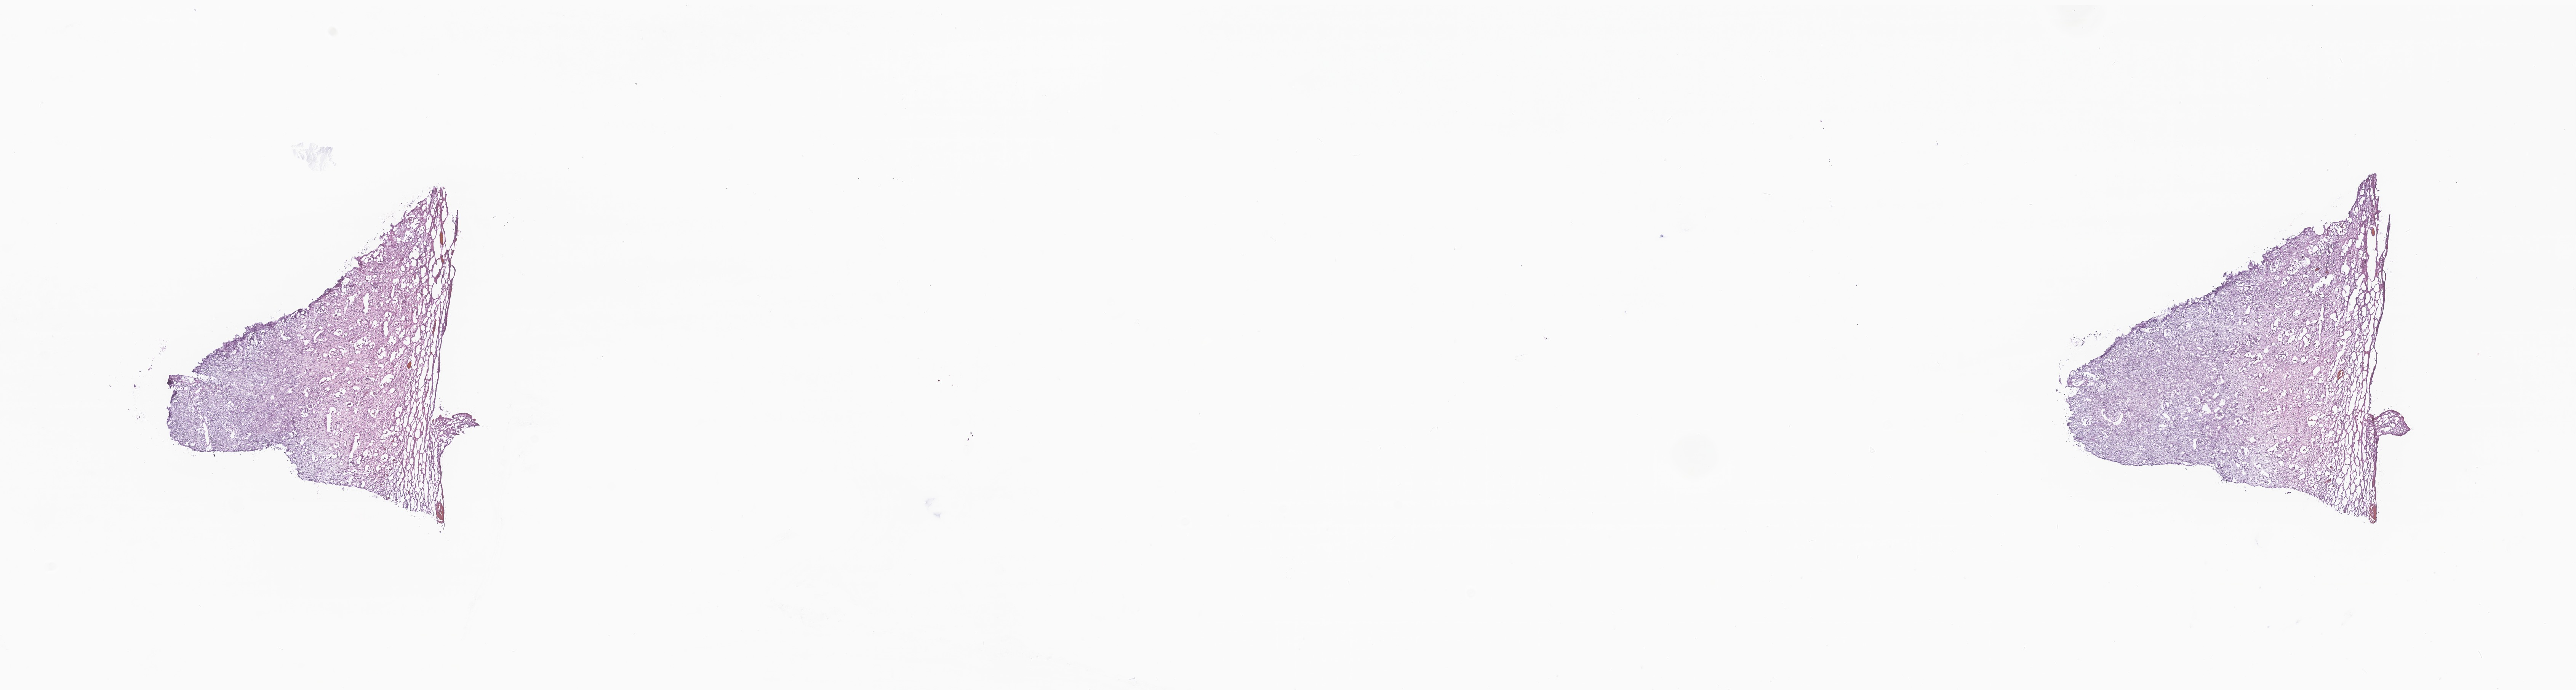
Whole-slide image, haematoxylin and eosin stain of tumor tissue from the brain — whole scanned area (about 28.5 x 7.6 mm) shown as a low-resolution overview; frozen section (OCT-embedded). Male patient, age 82 months (6 years 10 months).
Recorded diagnosis: Neoplasm, benign.